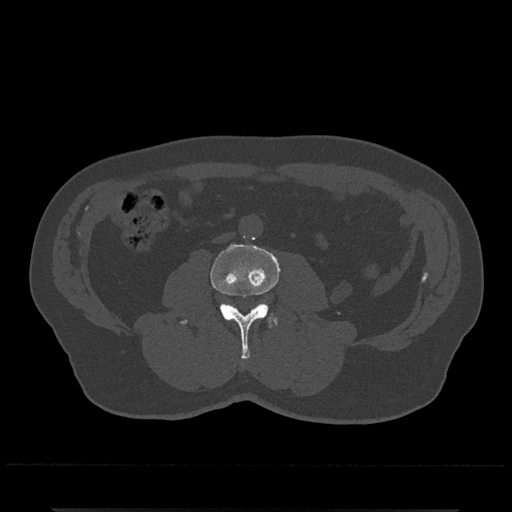
CT including the spine, one axial slice. Position 213 of 797 along the scan axis. Reconstruction kernel Br40s/3. 120 kVp. Bone window (W 1800 / L 400 HU). 0.5 mm slice thickness. 512 × 512 image matrix, field of view 393 × 393 mm. Male patient, age 67 years. Case-level facts recorded for this patient, not image findings: primary cancer: prostate.
Structures marked on this image (semi-automatic segmentation, software-assisted and operator-edited):
- L3 vertebra: bounding box <180,244,280,359> (left, top, right, bottom; pixels)
- L4 vertebra: <264,303,278,324>